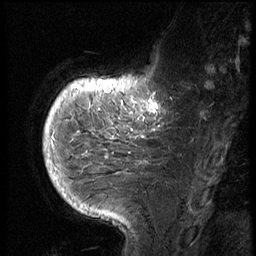
Breast MRI (dynamic contrast-enhanced), one sagittal slice. 3 images stored at this slice position (order not interpretable as contrast timing). 1.5 T. TE 4.2 ms, TR 8.9 ms. 2.5 mm slice thickness. 256 × 256 image matrix, field of view 200 × 200 mm. Patient: female, 56 years. Case-level facts recorded for this patient, not image findings: setting: breast cancer imaged before/during neoadjuvant chemotherapy.
Annotated regions visible in this slice (semi-automatic segmentation, software-assisted and operator-edited):
- analysis volume of interest (the breast-tissue region the enhancement analysis was run in; not a lesion): bounding box (x1, y1, x2, y2) in pixels: (114, 76, 177, 138)
- tumour enhancement mask (voxels above the 140 % enhancement threshold inside the analysis volume of interest): (146, 93, 160, 132)